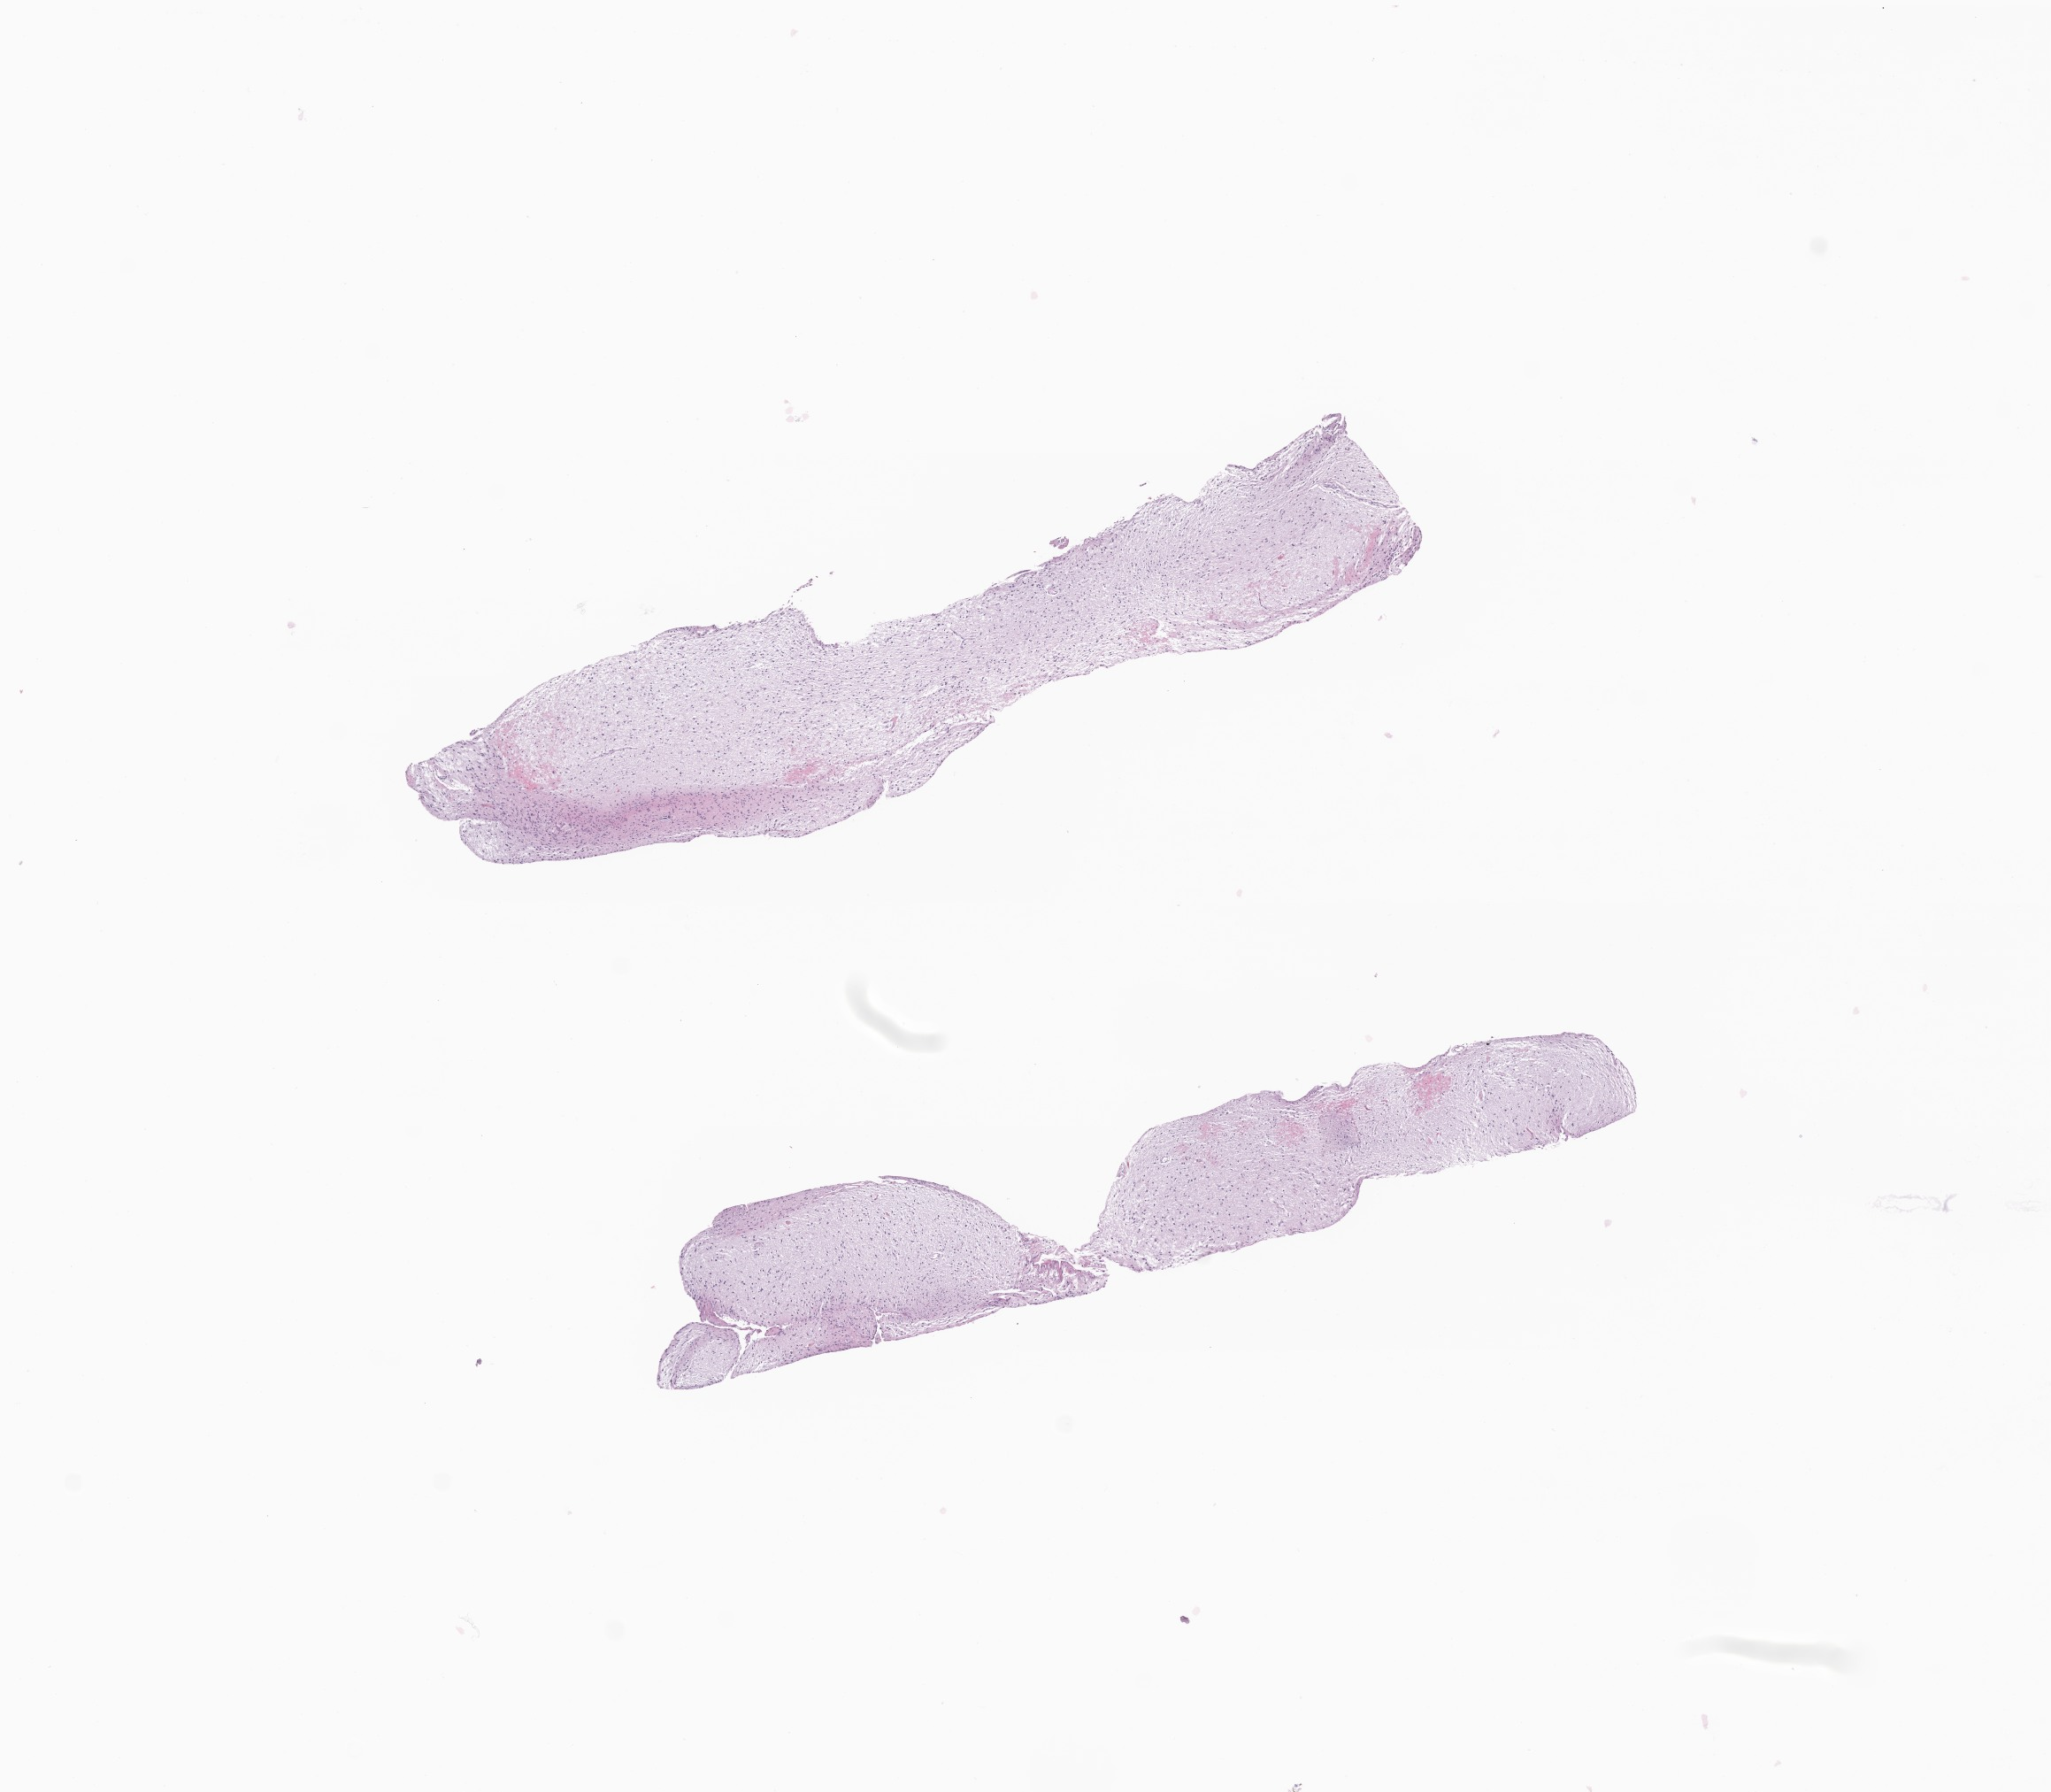
H&E whole-slide image of tumor tissue from the cerebellum, shown as a low-resolution overview of the whole scanned area (about 9.8 x 8.5 mm). Formalin-fixed paraffin-embedded section. Patient male; age 174 months (14 years 6 months).
Diagnosis: Glioma, malignant.